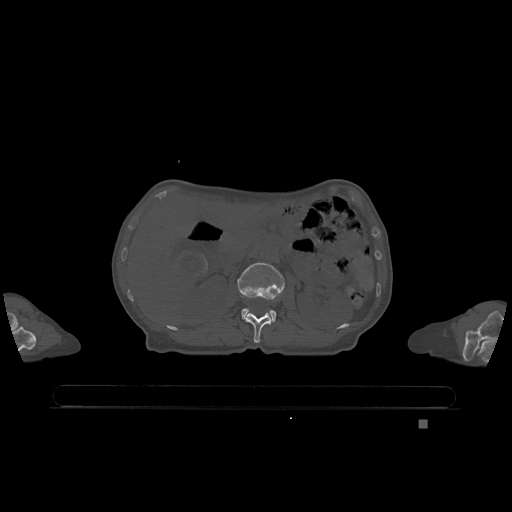
CT including the spine, one axial slice. Slice 448 of 1317 in the series (ordered by position). Bone window (W 1800 / L 400 HU). 0.5 mm slice thickness. 512 × 512 image matrix, field of view 500 × 500 mm. Female patient, age 74 years. From the clinical record (not read from this slice): primary cancer: lung.
Structures marked on this image (semi-automatic segmentation, software-assisted and operator-edited):
- L1 vertebra: box from (x=245, y=313) to (x=271, y=343) px
- L2 vertebra: (x=238, y=263)–(x=285, y=322)